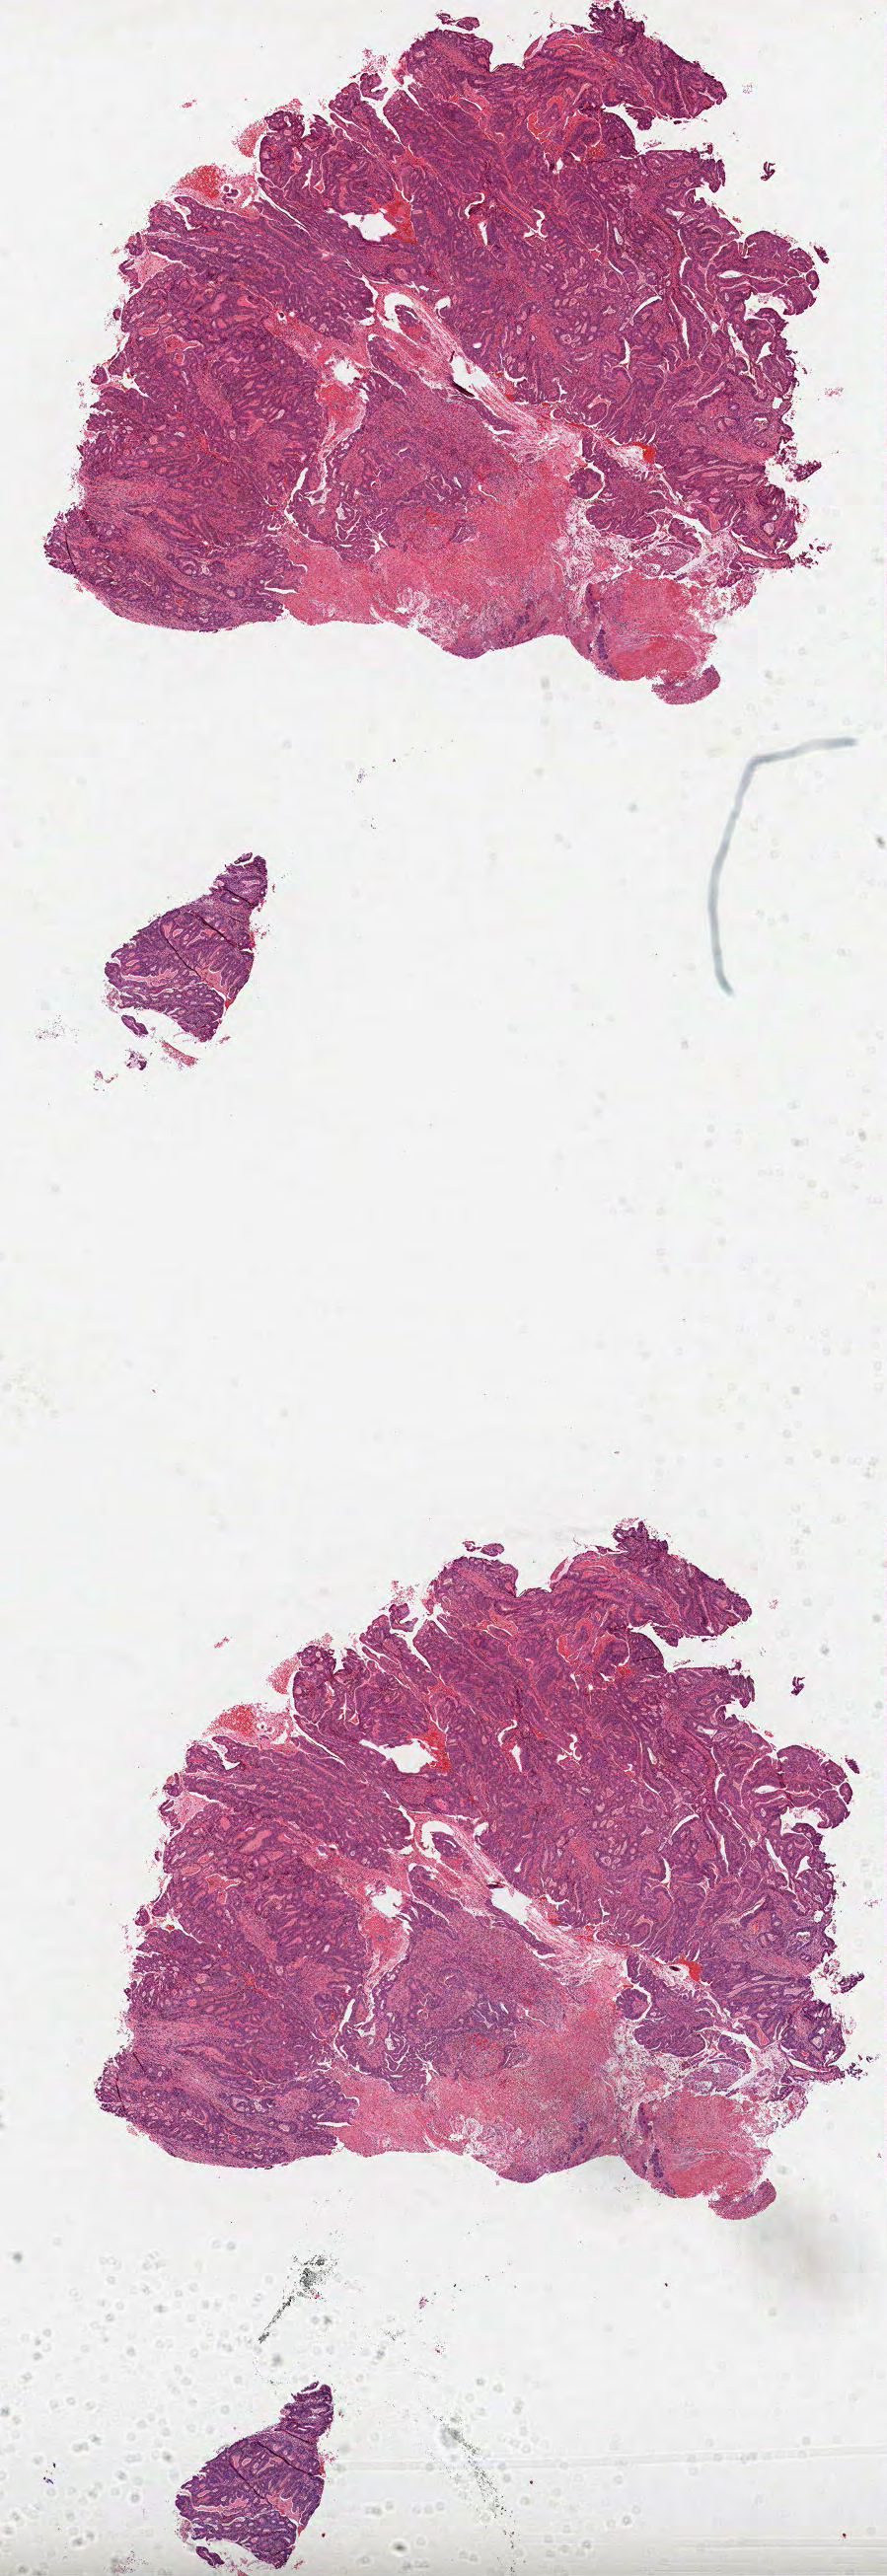
Hematoxylin and eosin (H&E) stained whole-slide image, low-resolution overview of the scanned area, about 7.3 x 21.1 mm (from a 40x scan); formalin-fixed paraffin-embedded (FFPE) diagnostic section; colon, primary tumour sample. Female patient; age at initial diagnosis 82 years.
- diagnosis: Adenocarcinoma, NOS (ascending colon)
- AJCC pathologic stage: IIIB
- lymph nodes positive (case pathology): 1 of 29 examined